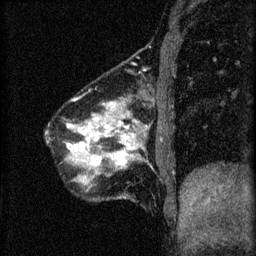
Breast MRI (dynamic contrast-enhanced), one sagittal slice. Slice 14 of 60 in the series (ordered by position). 3 images stored at this slice position (order not interpretable as contrast timing). 1.5 T. TE 4.2 ms, TR 8.2 ms. 2 mm slice thickness. 256 × 256 image matrix, field of view 180 × 180 mm. Female patient, age 40 years.
Annotated regions visible in this slice (semi-automatic segmentation, software-assisted and operator-edited):
- analysis volume of interest (the breast-tissue region the enhancement analysis was run in; not a lesion): bounding box <48,92,167,199> (left, top, right, bottom; pixels)
- tumour enhancement mask (voxels above the 70 % enhancement threshold inside the analysis volume of interest): <68,100,135,167>